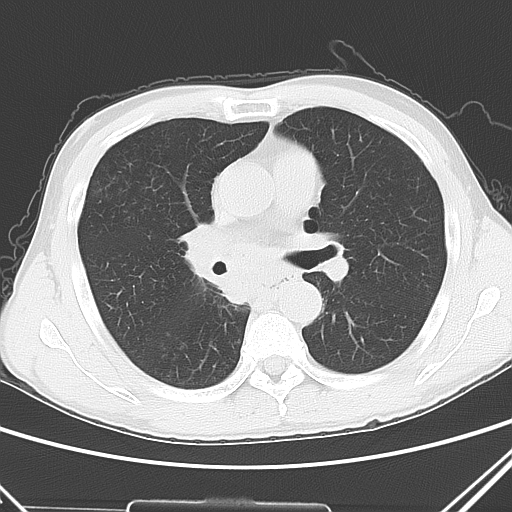
Chest CT, one axial slice. Slice 27 of 51 in the series (ordered by position). 120 kVp. Lung window (W 1500 / L -600 HU). 512 × 512 image matrix, field of view 327 × 327 mm. Patient: male, 52 years. From the clinical record (not read from this slice): clinical TNM (as recorded): T2a N0 M1c.
Structures marked on this image (bounding box drawn by a radiologist):
- lung tumour (recorded histology: squamous cell carcinoma): bounding box <175,219,252,324> (left, top, right, bottom; pixels)